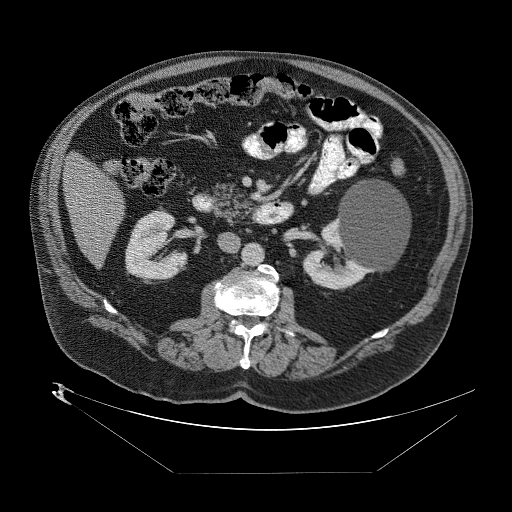
Contrast-enhanced abdominal CT (liver protocol), one axial slice; slice 16 of 89 in the series (ordered by position); reconstruction kernel STANDARD; 140 kVp; one of 2 acquisitions stored at this slice position; soft-tissue window (W 400 / L 40 HU); 2.5 mm slice thickness; 512 × 512 image matrix, field of view 480 × 480 mm. Case-level facts recorded for this patient, not image findings: diagnosis: hepatocellular carcinoma (patient treated with transarterial chemoembolisation; whether this scan precedes or follows treatment is not stated here); TNM stage (as recorded): Stage-II; Child-Pugh class: B; tumour size: 4 cm.
Annotated regions visible in this slice (semi-automatic segmentation, software-assisted and operator-edited):
- abdominal aorta: bounding box [x1, y1, x2, y2] px = [244, 243, 265, 266]
- liver parenchyma outside the tumour (the mass and vessels are separate outlines, so this box may not span the whole liver): [62, 148, 124, 258]